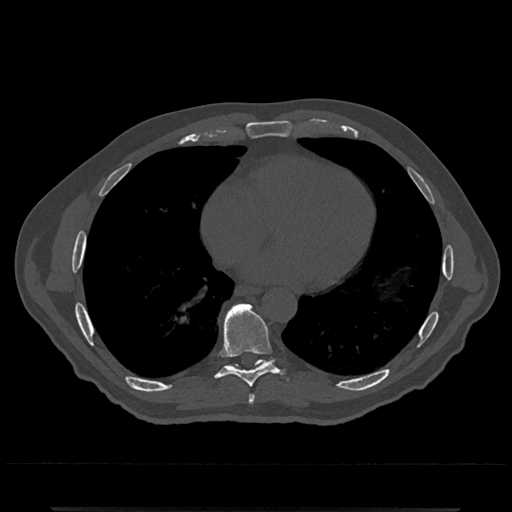
CT including the spine, one axial slice. Slice 662 of 797 in the series (ordered by position). Reconstruction kernel Br40s/3. 120 kVp. Bone window (W 1800 / L 400 HU). 0.5 mm slice thickness. 512 × 512 image matrix, field of view 393 × 393 mm. Male patient, age 67 years. From the clinical record (not read from this slice): primary cancer: prostate.
Structures marked on this image (semi-automatic segmentation, software-assisted and operator-edited):
- T7 vertebra: bounding box [x1, y1, x2, y2] px = [248, 395, 255, 404]
- T8 vertebra: [218, 303, 279, 387]
- T9 vertebra: [225, 358, 276, 368]